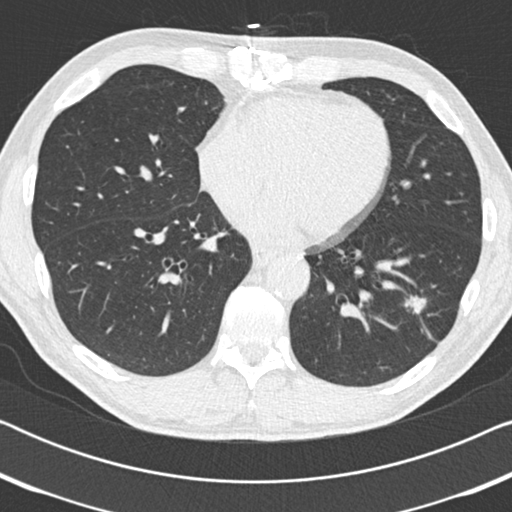
Low-dose screening chest CT, one axial slice; position 74 of 186 along the scan axis; lung window (W 1500 / L -600 HU); 2 mm slice thickness; 512 × 512 image matrix, field of view 330 × 330 mm.
Annotated regions visible in this slice (expert manual segmentation):
- lesion 1 (tumor, lower lobe of left lung): bounding box [x1, y1, x2, y2] px = [405, 296, 427, 312]